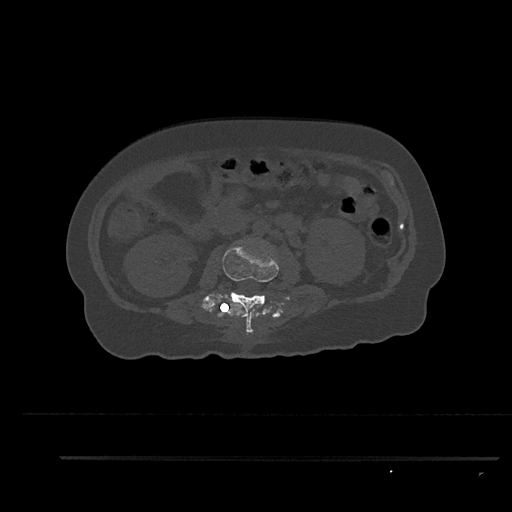
CT including the spine, one axial slice. Position 139 of 797 along the scan axis. Reconstruction kernel Br40s/3. Bone window (W 1800 / L 400 HU). 512 × 512 image matrix, field of view 408 × 408 mm. Female patient, age 44 years. From the clinical record (not read from this slice): primary cancer: renal; vertebrae with lytic lesions (as recorded): L1.
Outlined on this slice (semi-automatically segmented with operator editing):
- L2 vertebra: bounding box [x1, y1, x2, y2] px = [223, 241, 279, 335]